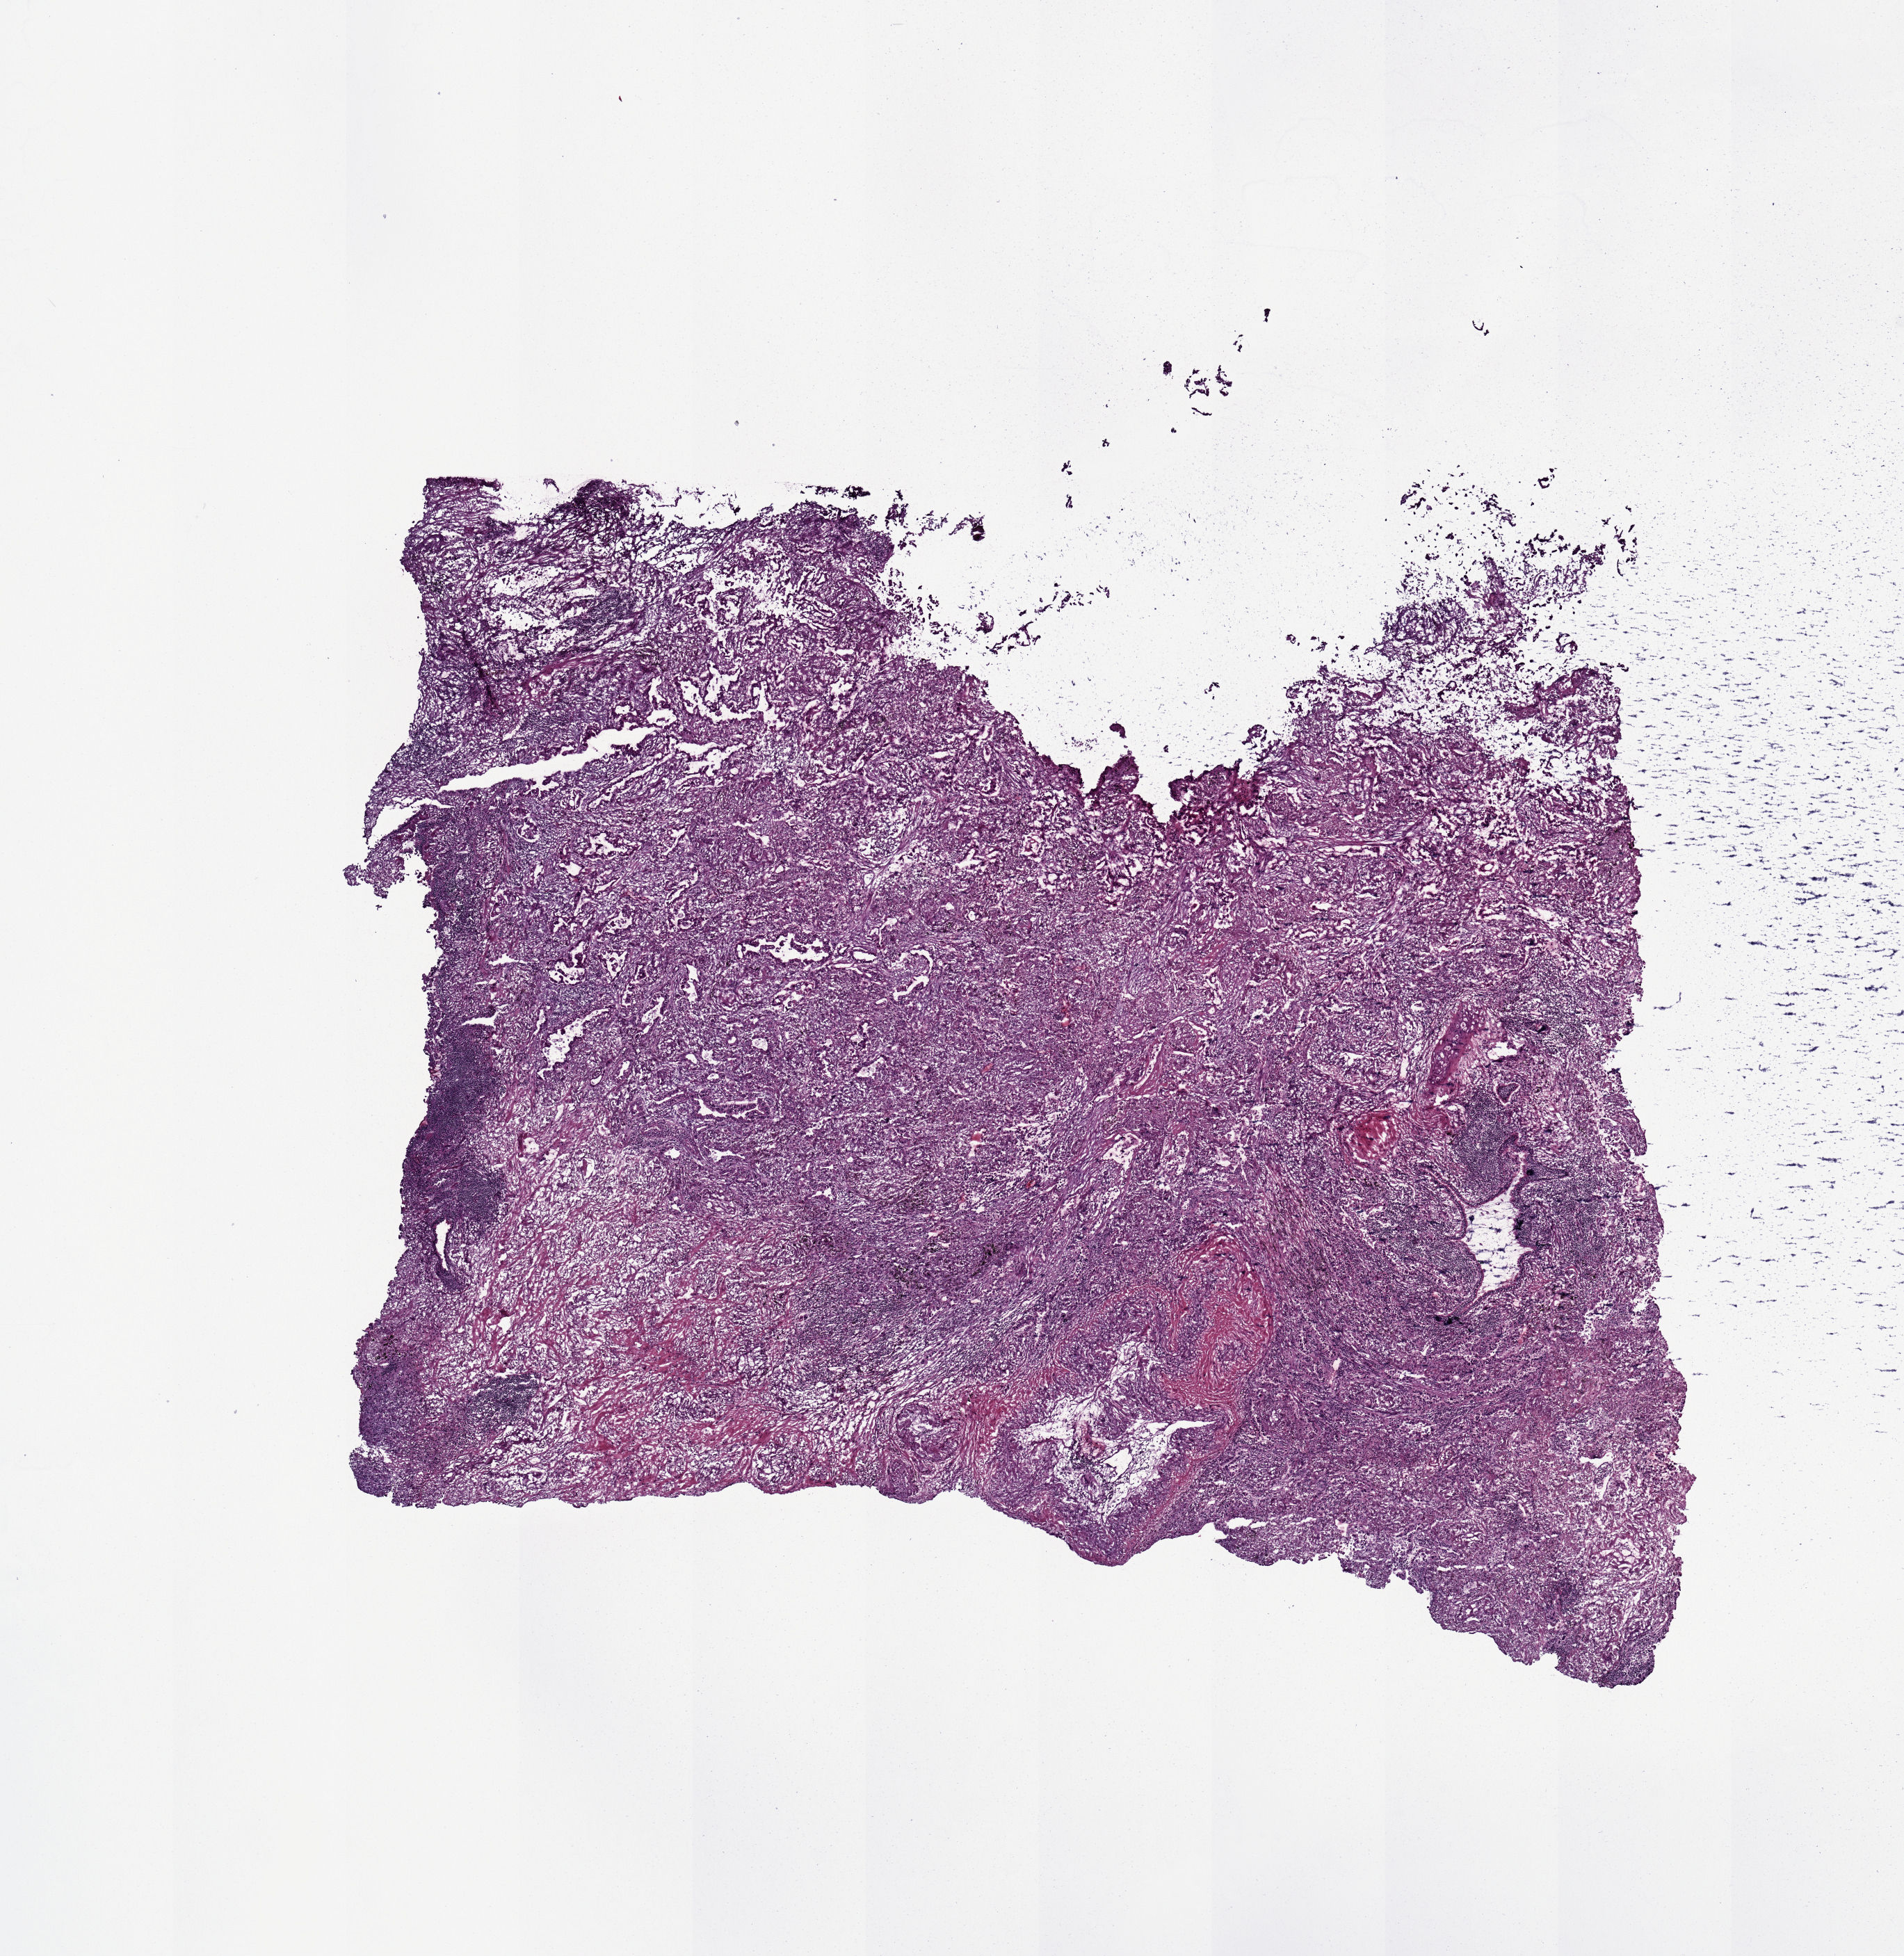
Whole-slide histology image, H&E-stained — a low-resolution overview of the entire scanned area, about 10.8 x 11.1 mm (slide scanned at 20x); tumour tissue sample, sampled site: lung. Female, 72 y/o.
Diagnosis: Adenocarcinoma, NOS.